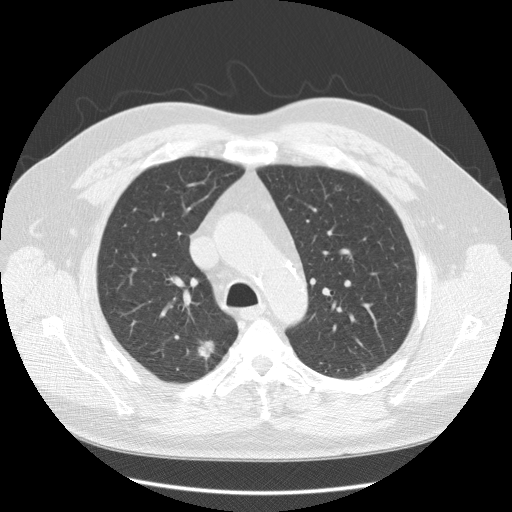
Axial slice from a low-dose chest CT screening exam; first (baseline) screen; lung window (W 1500 / L -600 HU); 2.5 mm slice thickness; standard (soft-tissue) reconstruction kernel (STANDARD); 120 kVp; 512 × 512 image matrix. Male, age 55 years at enrolment. Former smoker at enrolment.
Expert reader's lesion annotation, bounding box (x1, y1, x2, y2) in pixels: (183, 327, 232, 377). The screening reader recorded 2 non-calcified nodules or masses ≥4 mm on this exam; which of them this box marks is not recorded. Official screen result: positive, change unspecified: nodule(s) >= 4 mm or enlarging nodule(s), mass(es), or other non-specific abnormalities suspicious for lung cancer. Lung cancer was diagnosed 84 days after this screen: large cell neuroendocrine carcinoma, right upper lobe, poorly differentiated (G3), stage IA (AJCC 6th edition), 18 mm at pathology.